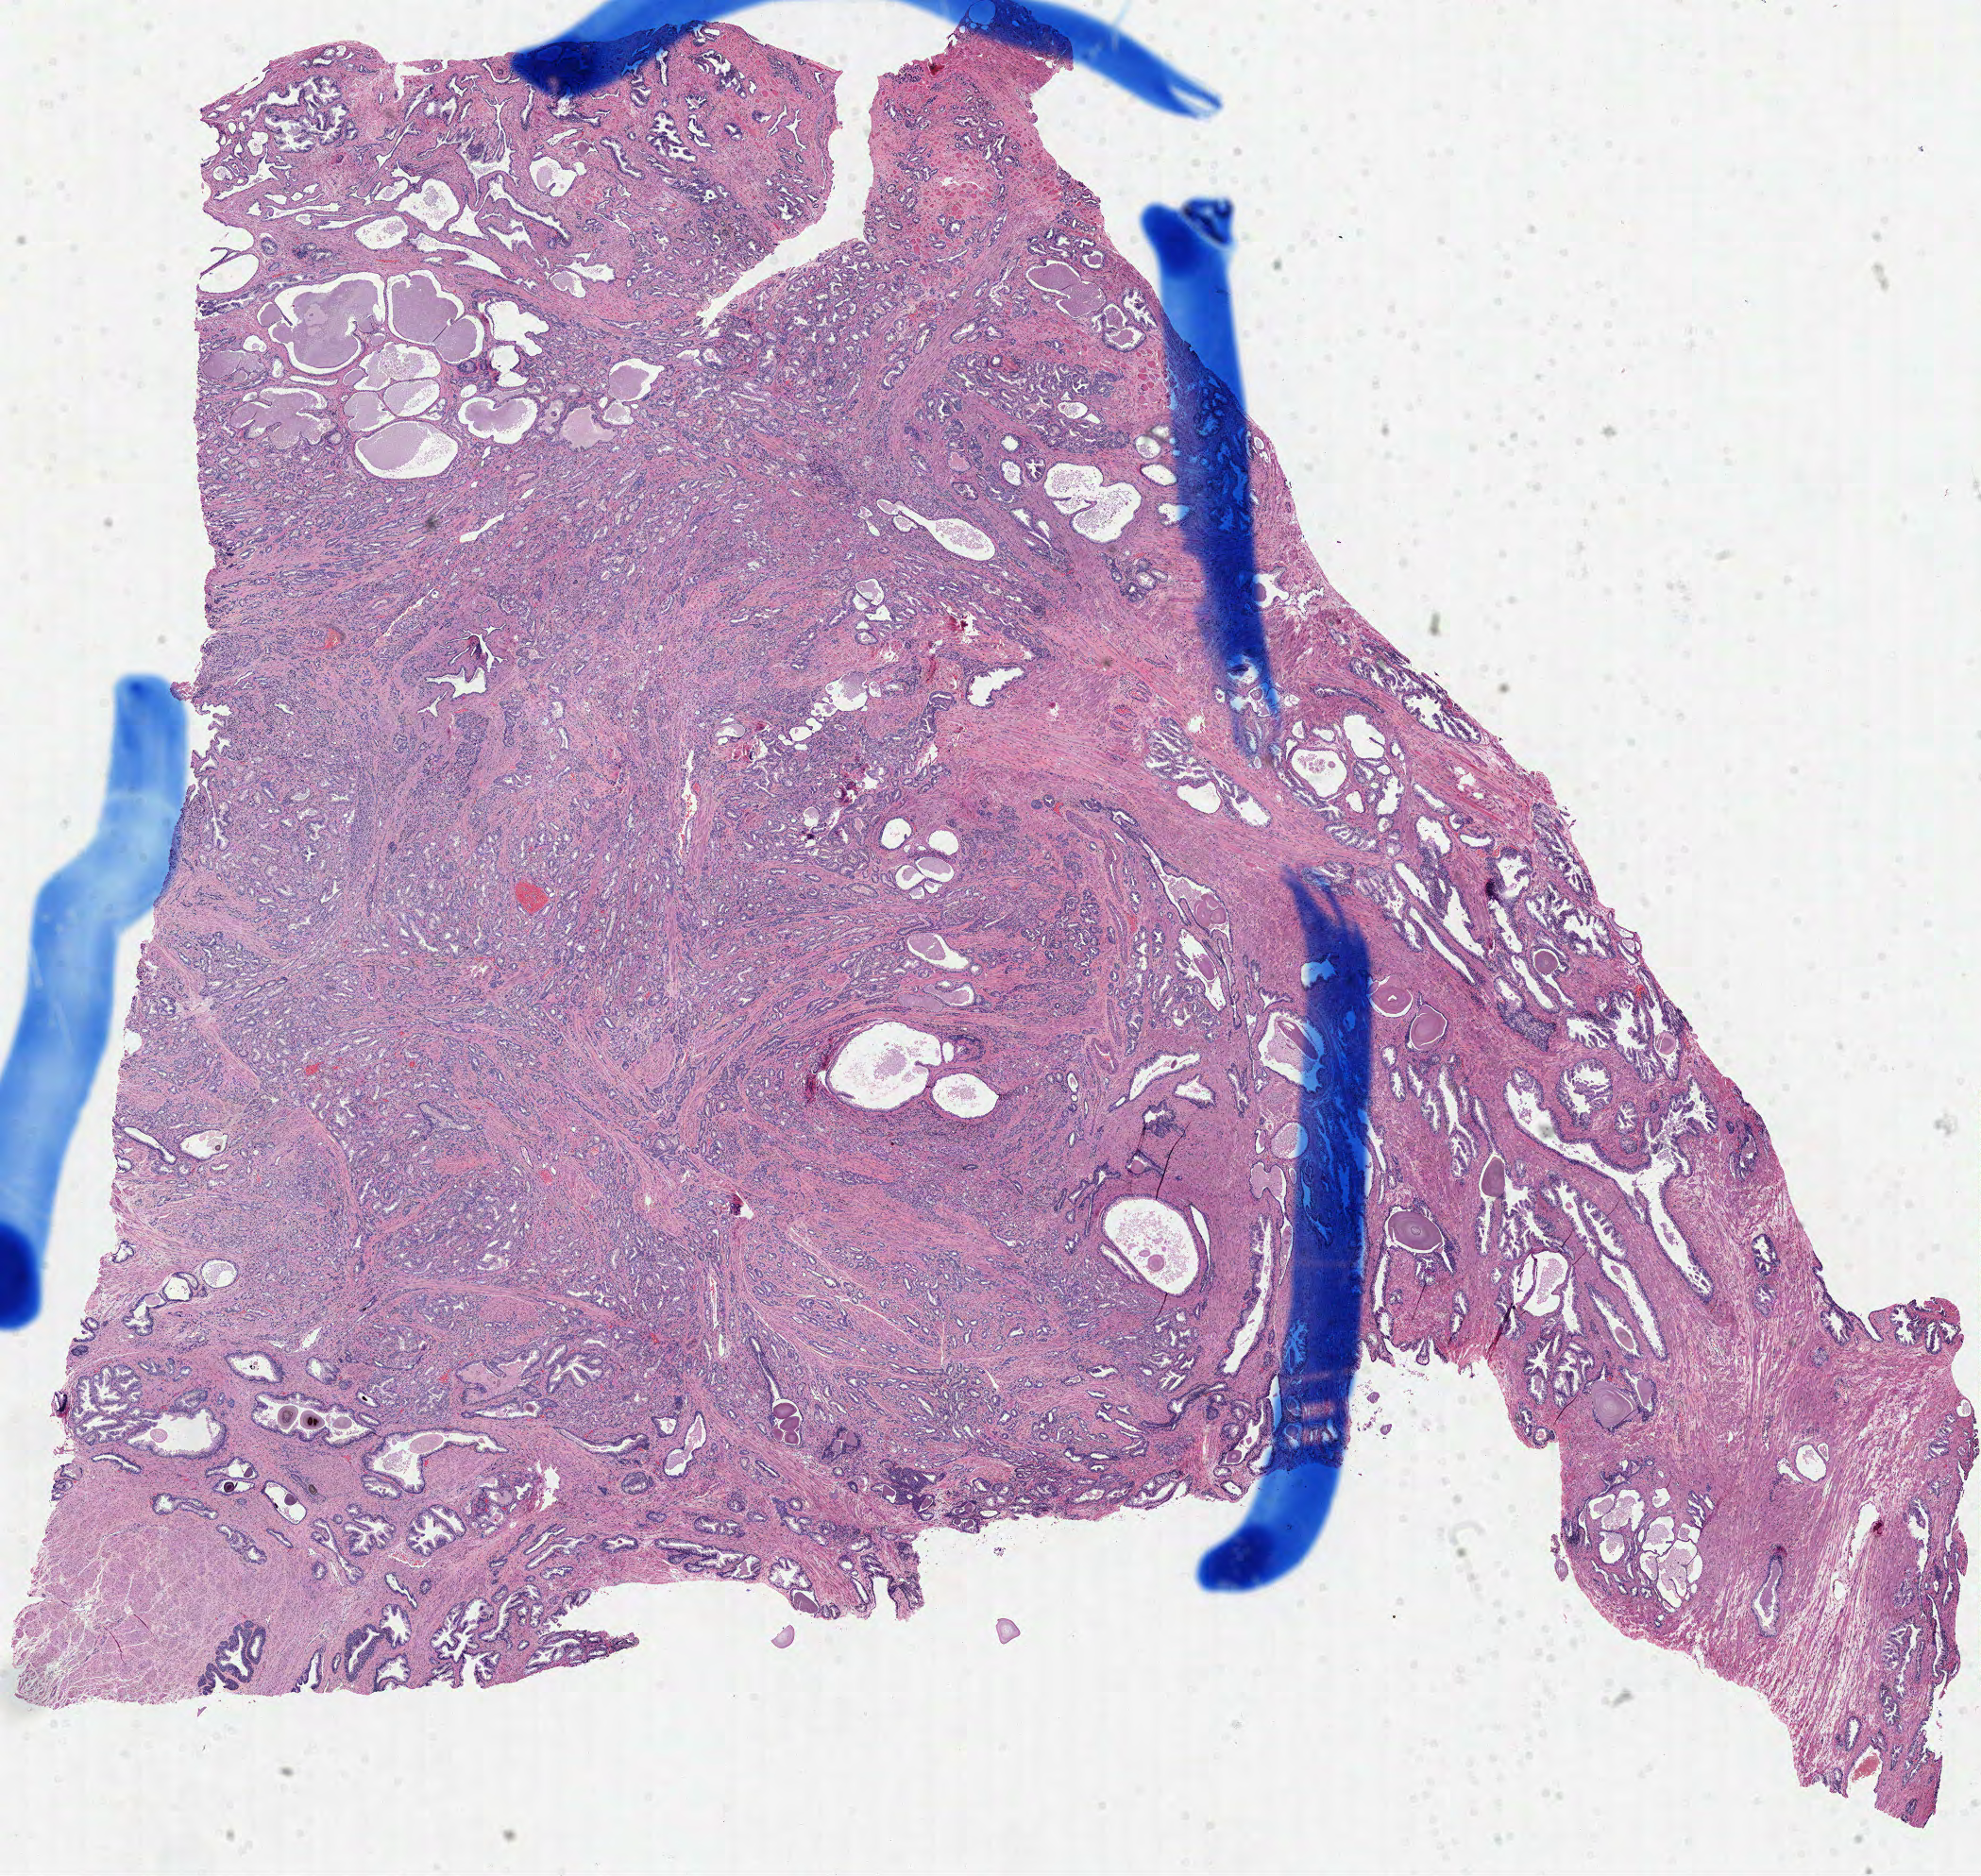
Digitized Hematoxylin and eosin (H&E) stained tissue section (whole slide) — shown as a low-resolution overview of the whole scanned area (about 16.9 x 16.0 mm, slide scanned at 40x); formalin-fixed paraffin-embedded (FFPE) diagnostic section; sample: primary tumour, prostate. Male patient; age at initial diagnosis 69 years. Gleason score: 7 (4+3).
Diagnosis: Acinar cell carcinoma (prostate gland). Lymph nodes positive (case pathology): 0 of 9 examined.